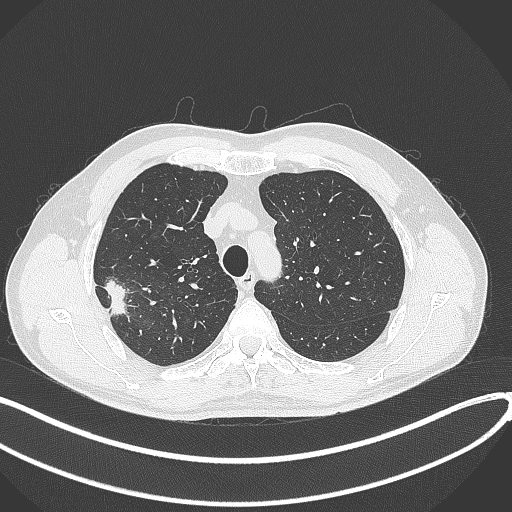
Chest CT, one axial slice; slice 324 of 381 in the series (ordered by position); reconstruction kernel B70f; lung window (W 1500 / L -600 HU); 1 mm slice thickness; 512 × 512 image matrix, field of view 400 × 400 mm. Male patient, age 62 years. Case-level facts recorded for this patient, not image findings: clinical TNM (as recorded): T1c N0 M0; histopathological grade: G2-3.
Outlined on this slice (rectangle marked by the reading radiologist):
- lung tumour (recorded histology: adenocarcinoma): box from (x=100, y=271) to (x=128, y=318) px